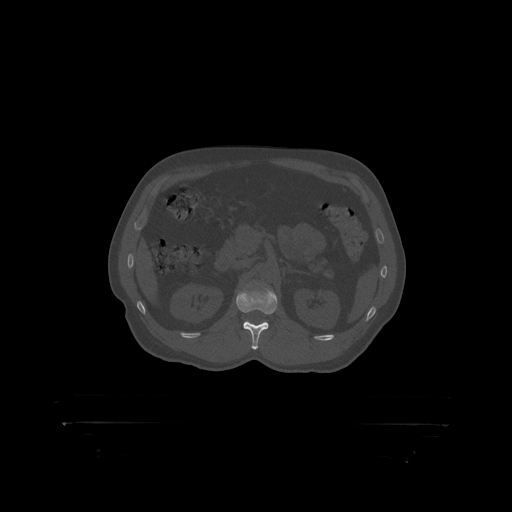
CT including the spine, one axial slice; position 318 of 399 along the scan axis; bone window (W 1800 / L 400 HU); 1.25 mm slice thickness; 512 × 512 image matrix, field of view 650 × 650 mm. Patient: male, 46 years. From the clinical record (not read from this slice): primary cancer: skin.
Outlined on this slice (semi-automatic segmentation, software-assisted and operator-edited):
- L1 vertebra: box from (x=237, y=288) to (x=278, y=315) px